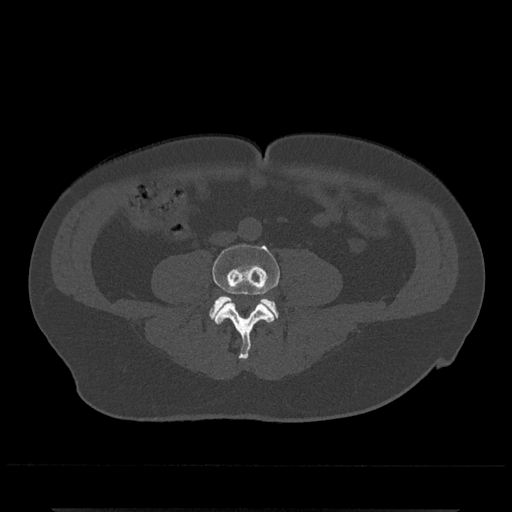
CT including the spine, one axial slice. Position 138 of 797 along the scan axis. Reconstruction kernel Br40s/3. 120 kVp. Bone window (W 1800 / L 400 HU). 0.5 mm slice thickness. 512 × 512 image matrix, field of view 393 × 393 mm. Male patient, age 67 years. Case-level facts recorded for this patient, not image findings: primary cancer: prostate.
Outlined on this slice (semi-automatically segmented with operator editing):
- L4 vertebra: bounding box <212,244,280,360> (left, top, right, bottom; pixels)
- L5 vertebra: <209,295,278,319>